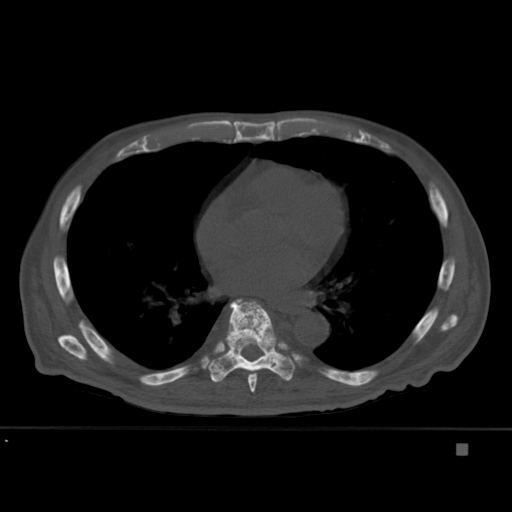
CT including the spine, one axial slice. Slice 267 of 451 in the series (ordered by position). Bone window (W 1800 / L 400 HU). 1.5 mm slice thickness. 512 × 512 image matrix, field of view 378 × 378 mm. Patient: male, 75 years. From the clinical record (not read from this slice): primary cancer: prostate.
Outlined on this slice (semi-automatic segmentation, software-assisted and operator-edited):
- T7 vertebra: bounding box <248,309,276,393> (left, top, right, bottom; pixels)
- T8 vertebra: <209,298,295,383>